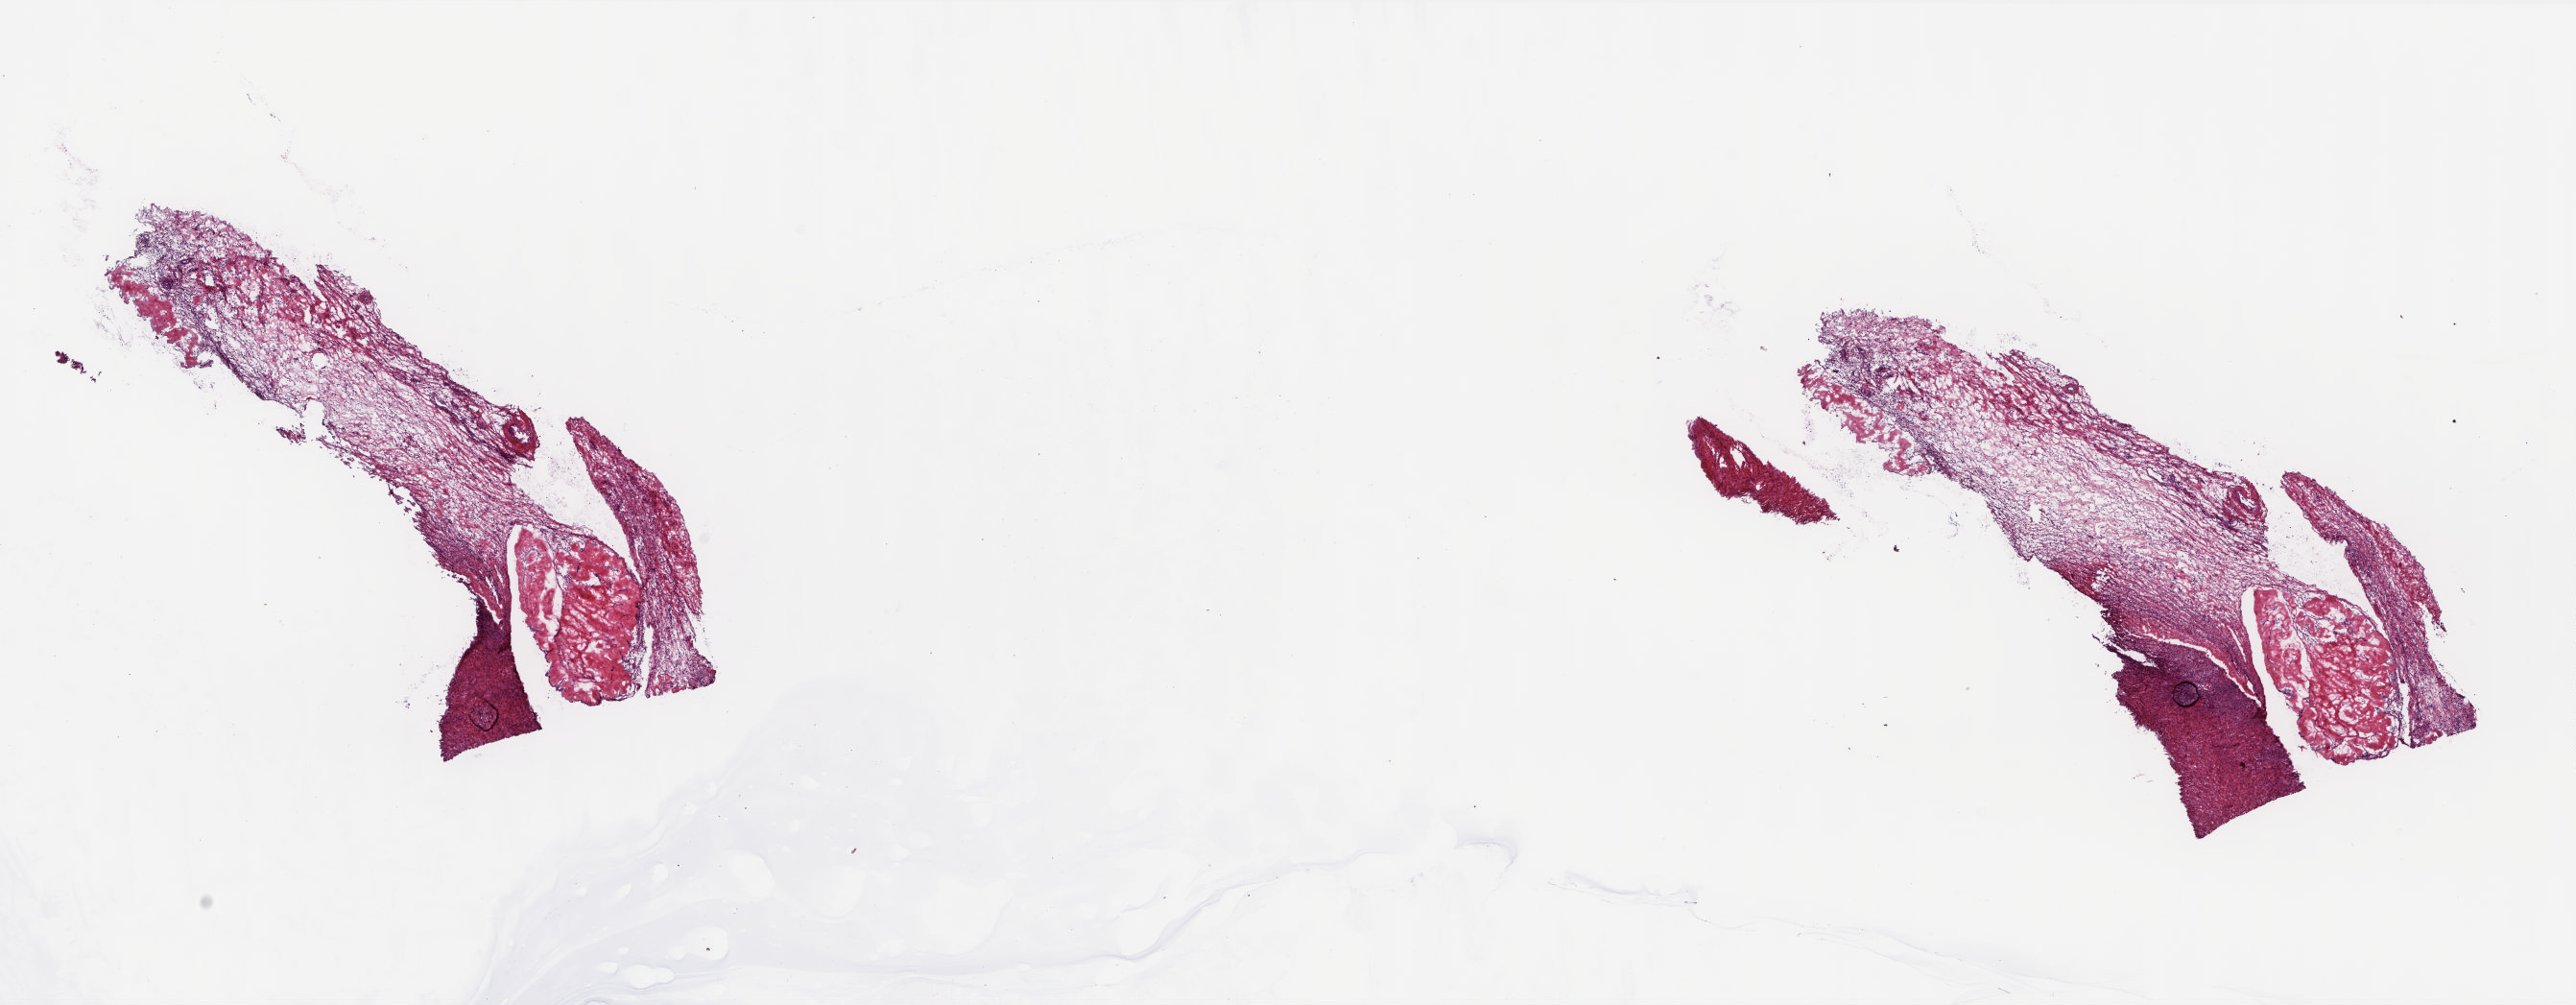
Digitized Hematoxylin and eosin (H&E) stained tissue section (whole slide) — shown as a low-resolution overview of the whole scanned area (about 21.6 x 8.4 mm); frozen section from the top of the tissue portion; solid tissue normal (non-tumour tissue) sample from the uterus. Female patient; age at initial diagnosis 51 years. Slide review estimates, as recorded: tumour cells 0%, tumour nuclei 0%, normal cells 90%, stromal cells 0%, necrosis 10%. Infiltration values recorded for this section: lymphocyte infiltration 10%, monocyte infiltration 10%, neutrophil infiltration 0%.
* this section: solid tissue normal (non-tumour) sample from the same patient
* patient diagnosis: Mullerian mixed tumor